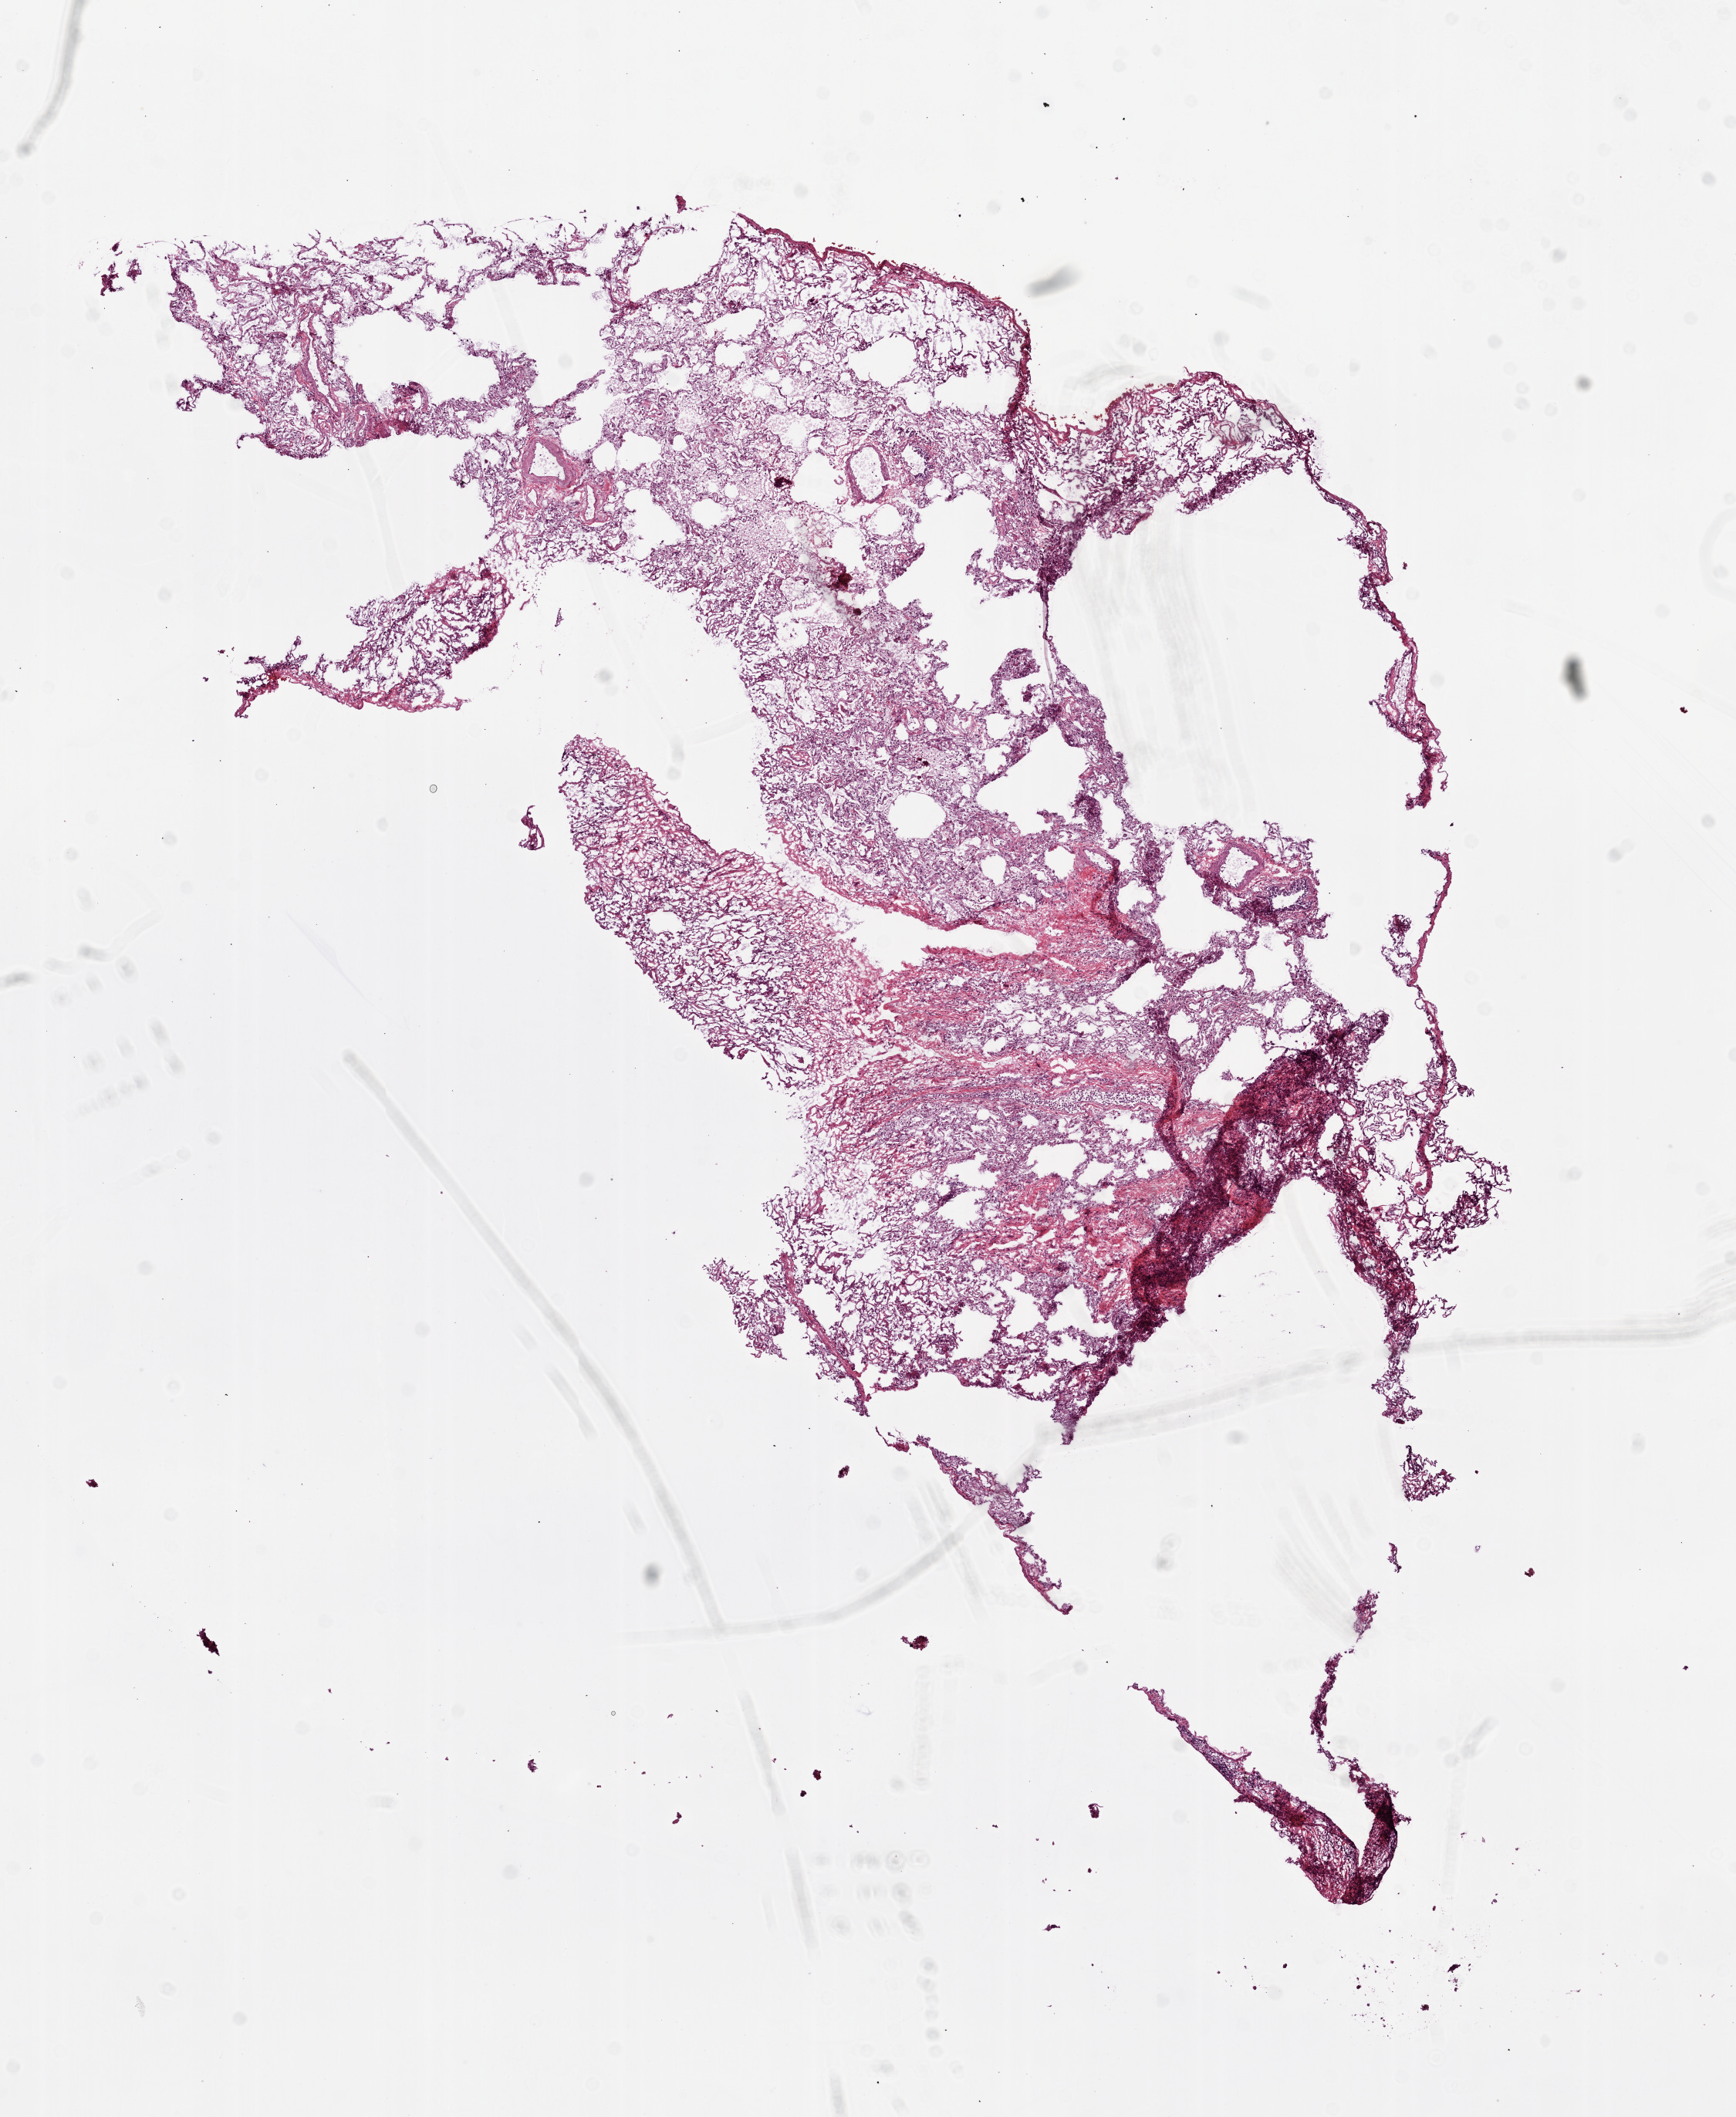
Digitized H&E-stained tissue section (whole slide), a low-resolution overview of the entire scanned area, about 9.0 x 11.0 mm; frozen section from the top of the tissue portion; sample: solid tissue normal (non-tumour tissue), lung. Female, age 69 years at initial diagnosis.
This section: solid tissue normal sample (biorepository sample class). Patient diagnosis: Adenocarcinoma, NOS (upper lobe, lung).